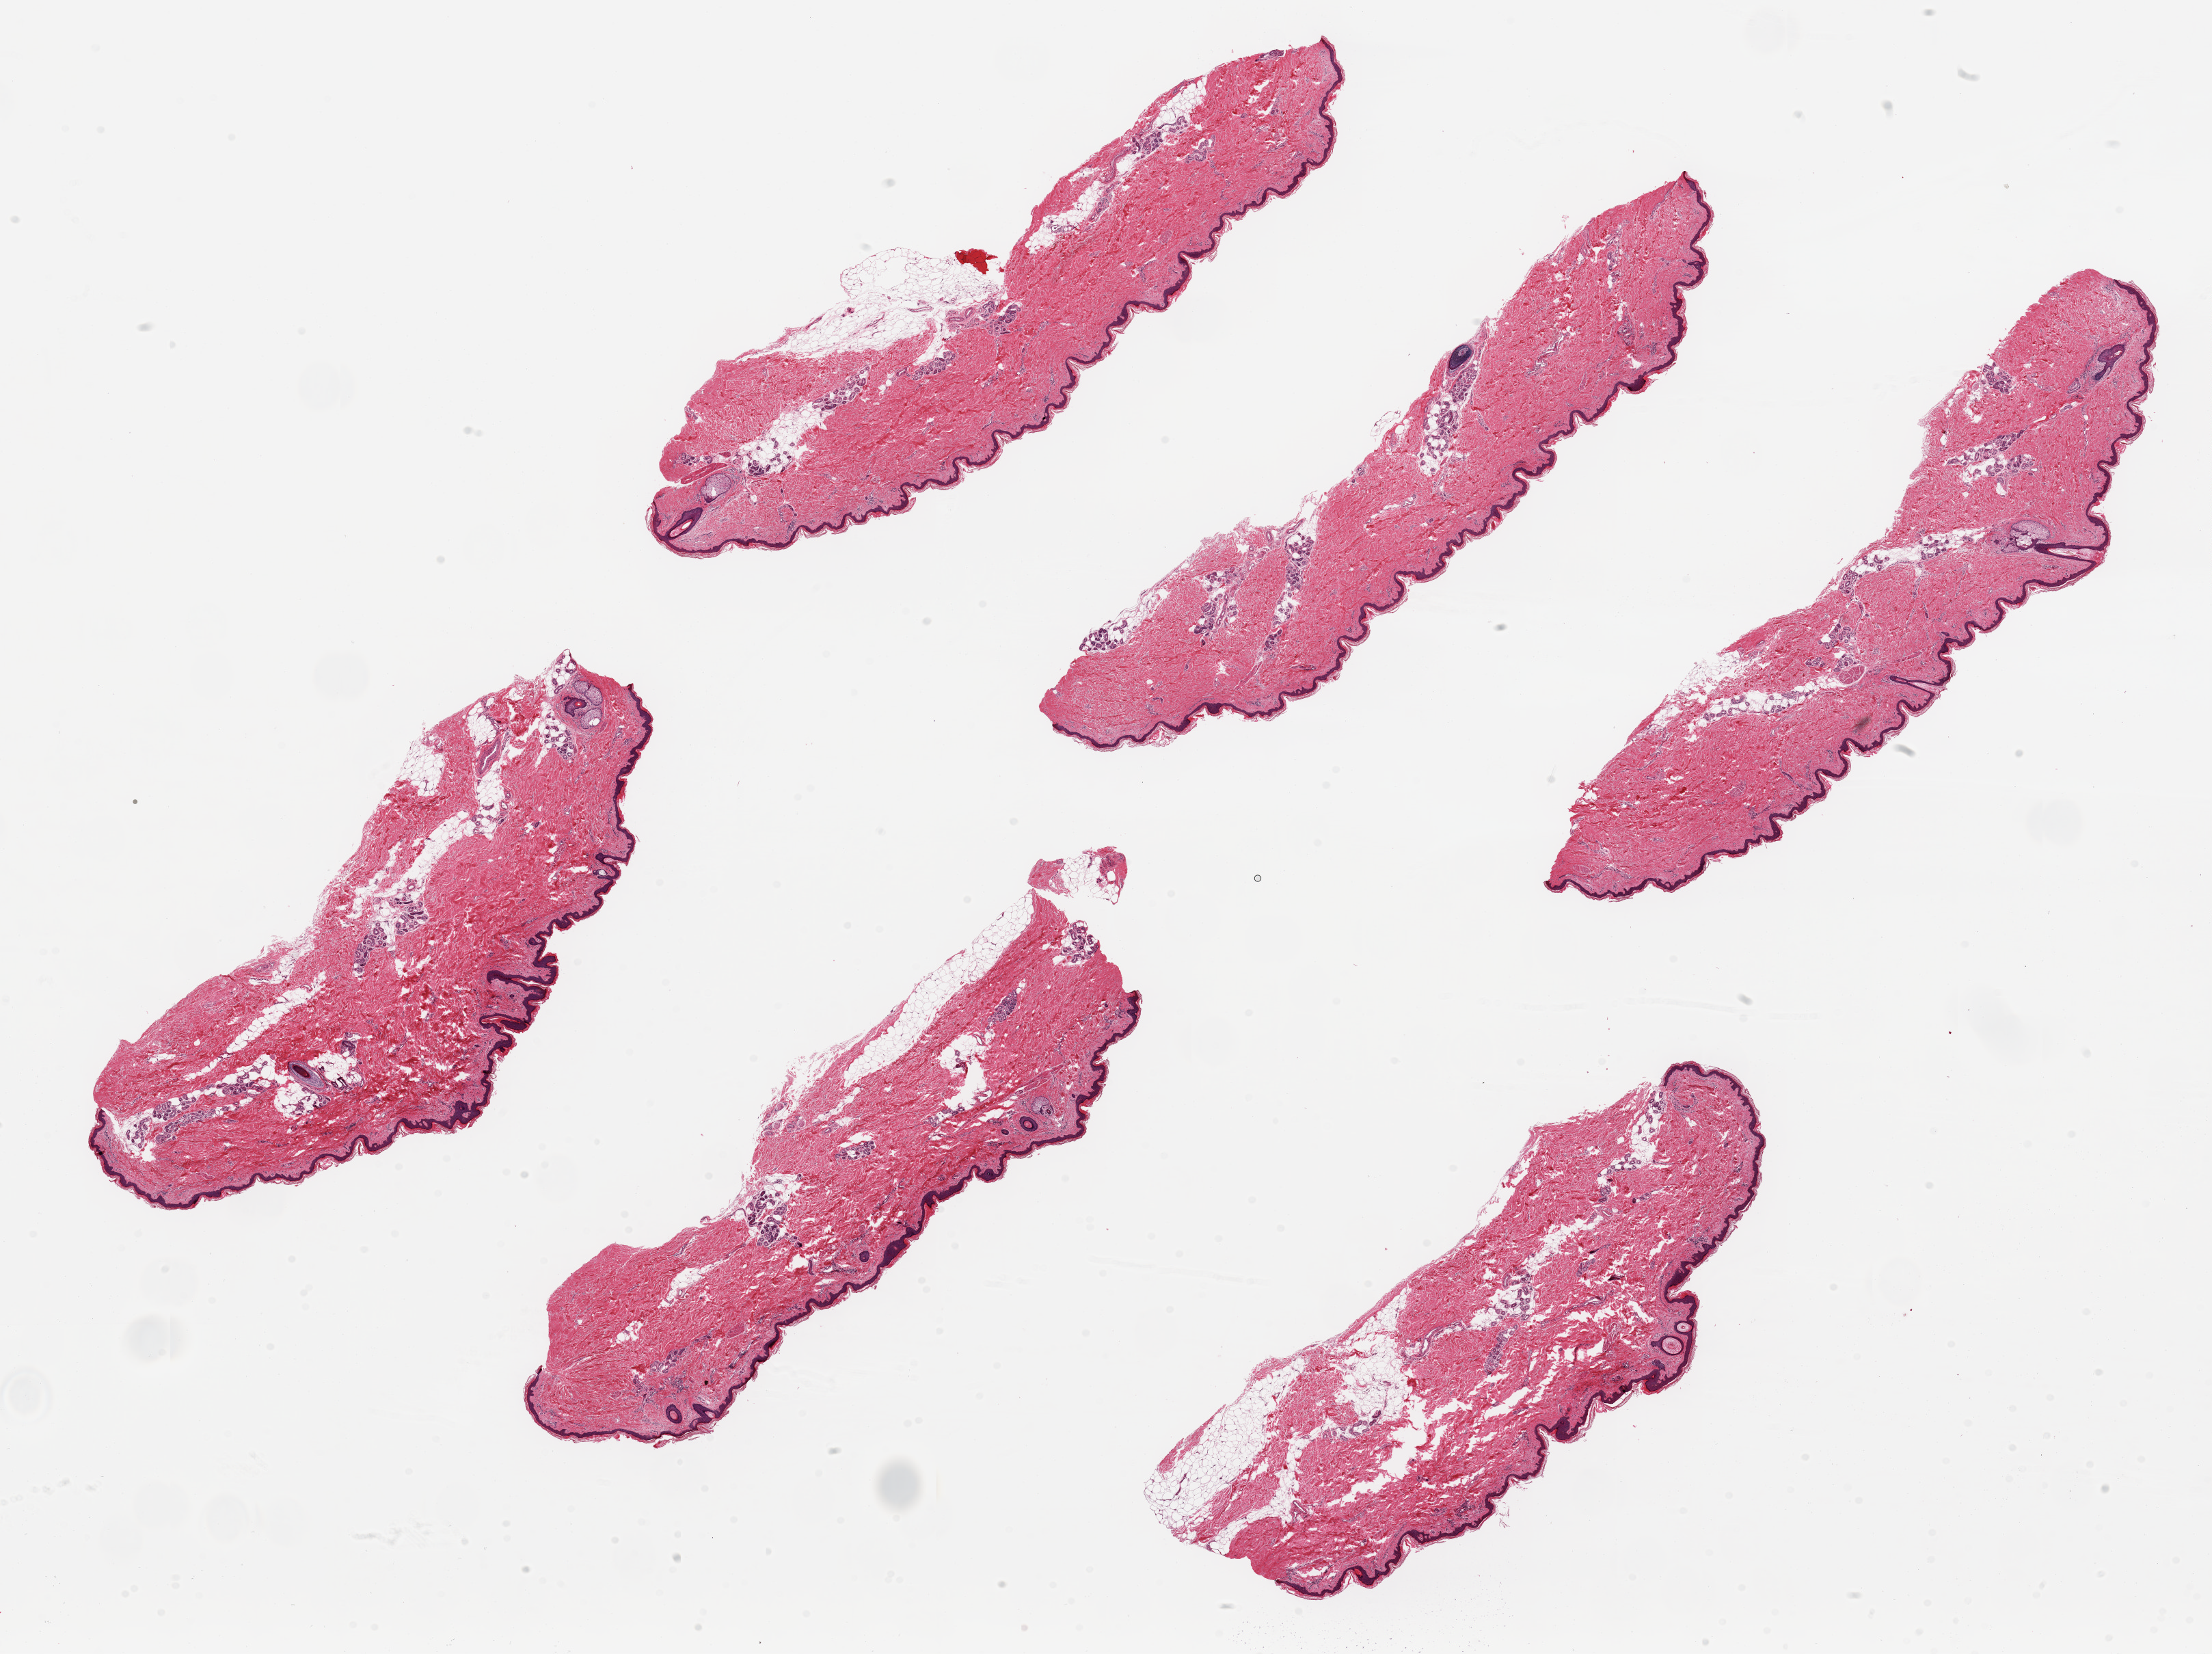
Digitized H&E-stained section — a low-resolution overview of the entire scanned area, about 25.6 x 19.1 mm. PAXgene-fixed, paraffin-embedded tissue. Target tissue: skin of lower leg. Tissue donor sample. Donor: male.
* pathologist's review note for this sample: 6 pieces, ~8.5x2mm. Squamous epithelium is 2-3% of thickness